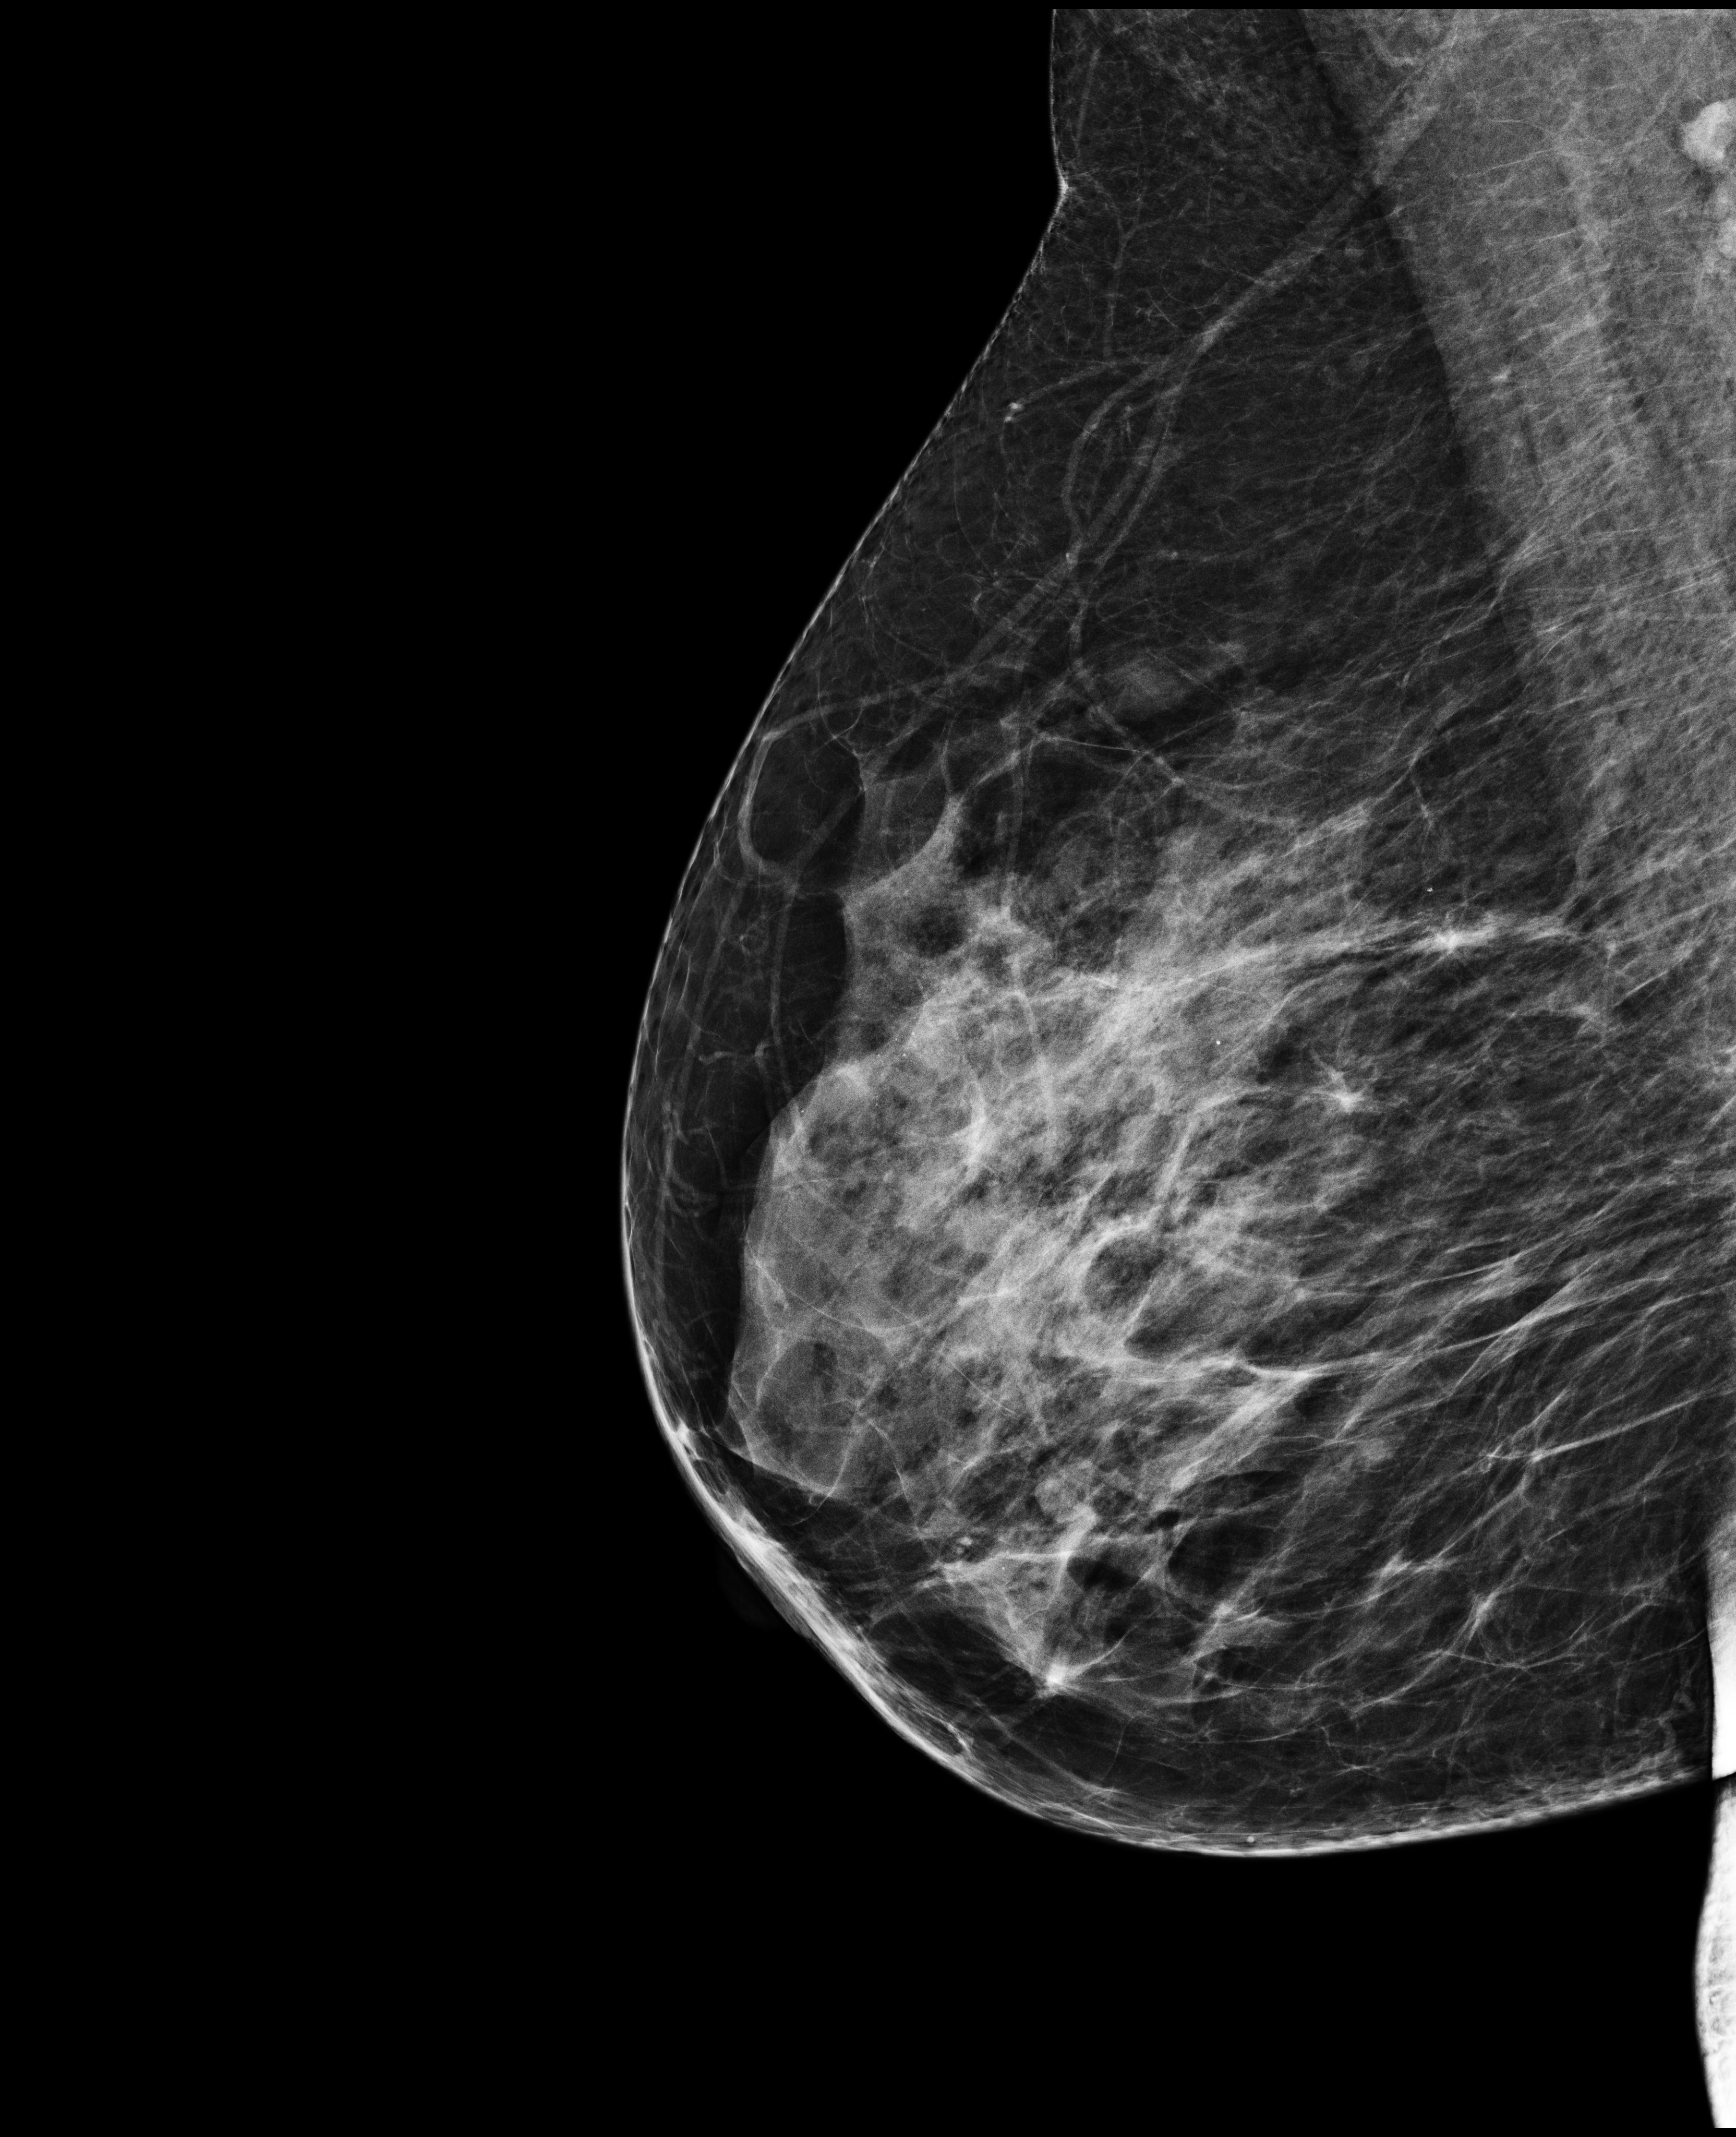
Full-field digital mammogram (FFDM), right breast, mediolateral oblique (MLO) view, annual screening mammography examination, system: Selenia Dimensions. Patient aged 48 years (female).
BI-RADS breast density category at the screening exam (both breasts, scale 1–4): 3. Final BI-RADS assessment for this screening round (tomosynthesis exam, both breasts): category 2. Recall: no recall after this screen.